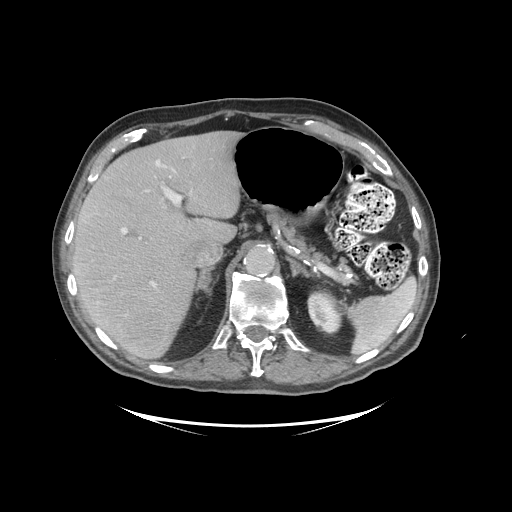
Contrast-enhanced abdominal CT (liver protocol), one axial slice. Position 67 of 99 along the scan axis. 140 kVp. Soft-tissue window (W 400 / L 40 HU). 2.5 mm slice thickness. 512 × 512 image matrix. Case-level facts recorded for this patient, not image findings: diagnosis: hepatocellular carcinoma (patient treated with transarterial chemoembolisation; whether this scan precedes or follows treatment is not stated here); TNM stage (as recorded): Stage-I; Child-Pugh class: A; tumour nodularity: uninodular.
Annotated regions visible in this slice (semi-automatic segmentation, software-assisted and operator-edited):
- liver parenchyma outside the tumour (the mass and vessels are separate outlines, so this box may not span the whole liver): box from (x=72, y=130) to (x=240, y=358) px
- liver vessels: (x=114, y=160)–(x=181, y=287)